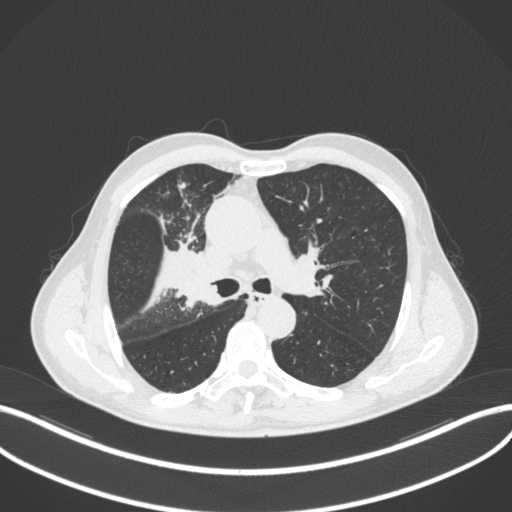
Chest CT, one axial slice. Position 311 of 490 along the scan axis. Reconstruction kernel B31f. Lung window (W 1500 / L -600 HU). 1 mm slice thickness. 512 × 512 image matrix, field of view 400 × 400 mm. Patient: male, 69 years. From the clinical record (not read from this slice): clinical TNM (as recorded): T2a N0 M0.
Outlined on this slice (bounding box drawn by a radiologist):
- lung tumour (recorded histology: adenocarcinoma): bounding box <170,255,216,313> (left, top, right, bottom; pixels)